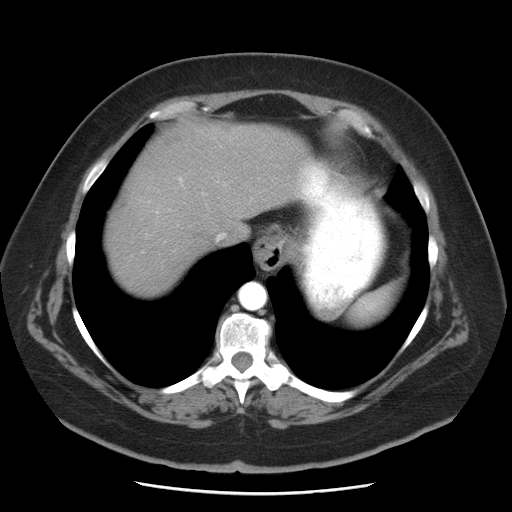
Contrast-enhanced abdominal CT, one axial slice. Position 41 of 55 along the scan axis. Reconstruction kernel STANDARD. 120 kVp. Intravenous contrast given. Soft-tissue window (W 400 / L 40 HU). 512 × 512 image matrix, field of view 380 × 380 mm. Female patient, age 52 years. Case-level facts recorded for this patient, not image findings: diagnosis: colorectal cancer liver metastases, imaged before liver resection.
Structures marked on this image (manually delineated by an expert):
- hepatic veins: bounding box [x1, y1, x2, y2] px = [217, 234, 225, 240]
- liver: [104, 121, 310, 296]
- planned liver remnant (the part of the liver to remain after resection): [104, 173, 200, 297]
- portal vein (with intrahepatic branches): [178, 177, 183, 186]
- liver metastasis: [217, 122, 236, 133]